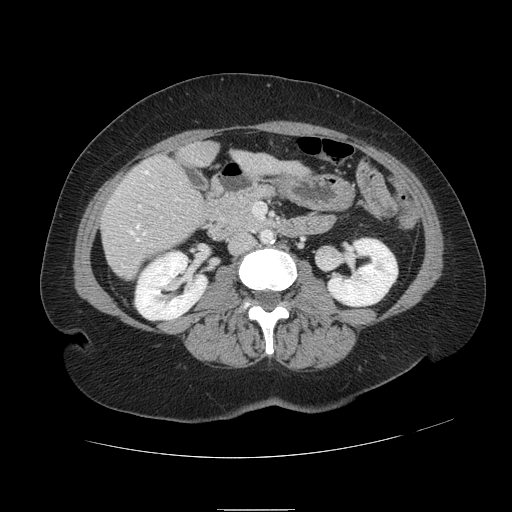
Contrast-enhanced abdominal CT, one axial slice. Slice 29 of 121 in the series (ordered by position). Intravenous contrast given. Soft-tissue window (W 400 / L 40 HU). 512 × 512 image matrix, field of view 400 × 400 mm. Female patient, age 52 years. Case-level facts recorded for this patient, not image findings: diagnosis: colorectal cancer liver metastases, imaged before liver resection.
Annotated regions visible in this slice (outlined manually by an expert reader):
- hepatic veins: box from (x=129, y=171) to (x=152, y=242) px
- liver: (x=101, y=144)–(x=282, y=279)
- planned liver remnant (the part of the liver to remain after resection): (x=181, y=144)–(x=284, y=171)
- portal vein (with intrahepatic branches): (x=138, y=205)–(x=141, y=209)